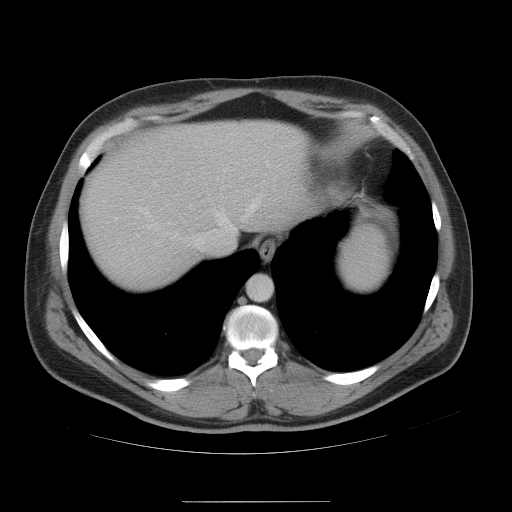
Contrast-enhanced abdominal CT, one axial slice; position 44 of 54 along the scan axis; 120 kVp; intravenous contrast given; soft-tissue window (W 400 / L 40 HU); 5 mm slice thickness; 512 × 512 image matrix. Male patient, age 40 years. From the clinical record (not read from this slice): diagnosis: colorectal cancer liver metastases, imaged before liver resection; multiple liver metastases: no; largest metastasis: 15 cm.
Outlined on this slice (manually delineated by an expert):
- hepatic veins: bounding box (x1, y1, x2, y2) in pixels: (137, 195, 263, 247)
- liver: (80, 121, 325, 293)
- planned liver remnant (the part of the liver to remain after resection): (162, 121, 324, 259)